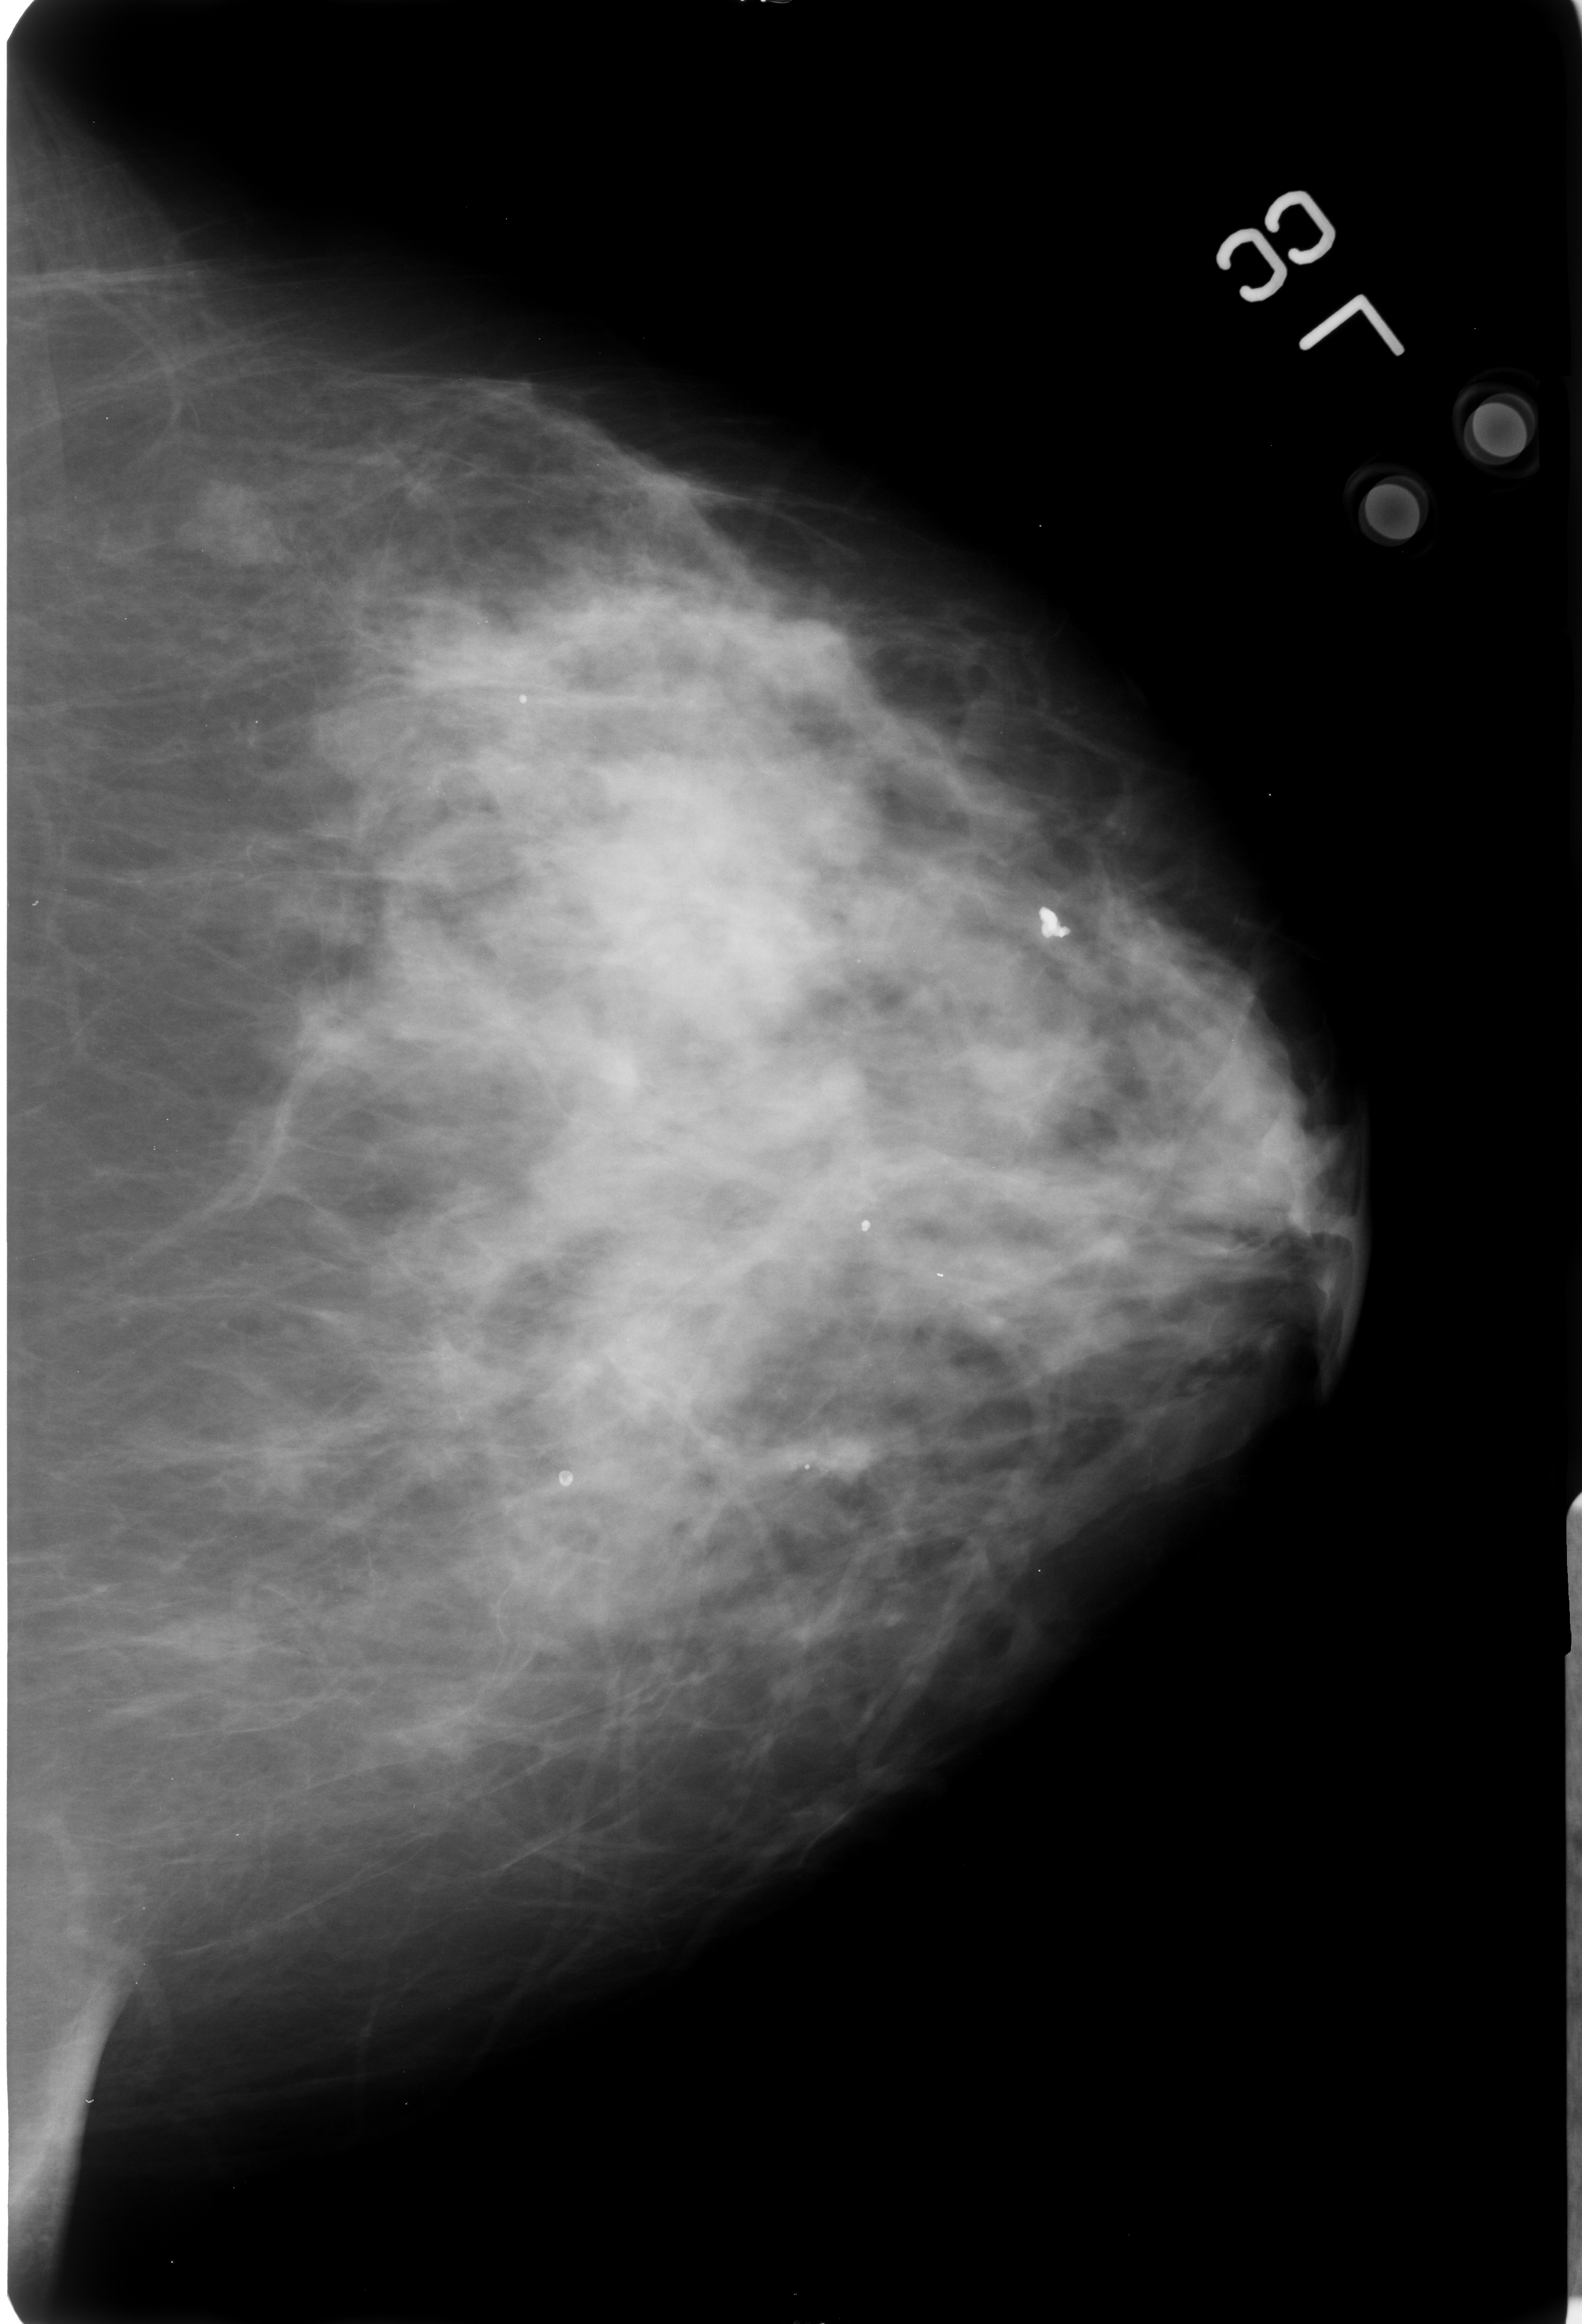
Digitized screen-film mammogram; left breast; craniocaudal (CC) view; breast composition: heterogeneously dense (BI-RADS density category 3 of 4); 1582 × 2324 image matrix.
Expert-marked regions of interest on this image (one box per marked abnormality):
- calcifications, morphology round and regular / lucent center / dystrophic, distribution diffusely scattered; BI-RADS assessment category 2; benign; no additional work-up was recommended (outcome (as recorded, no biopsy): benign without callback): bounding box (x1, y1, x2, y2) in pixels: (1029, 903, 1075, 949)